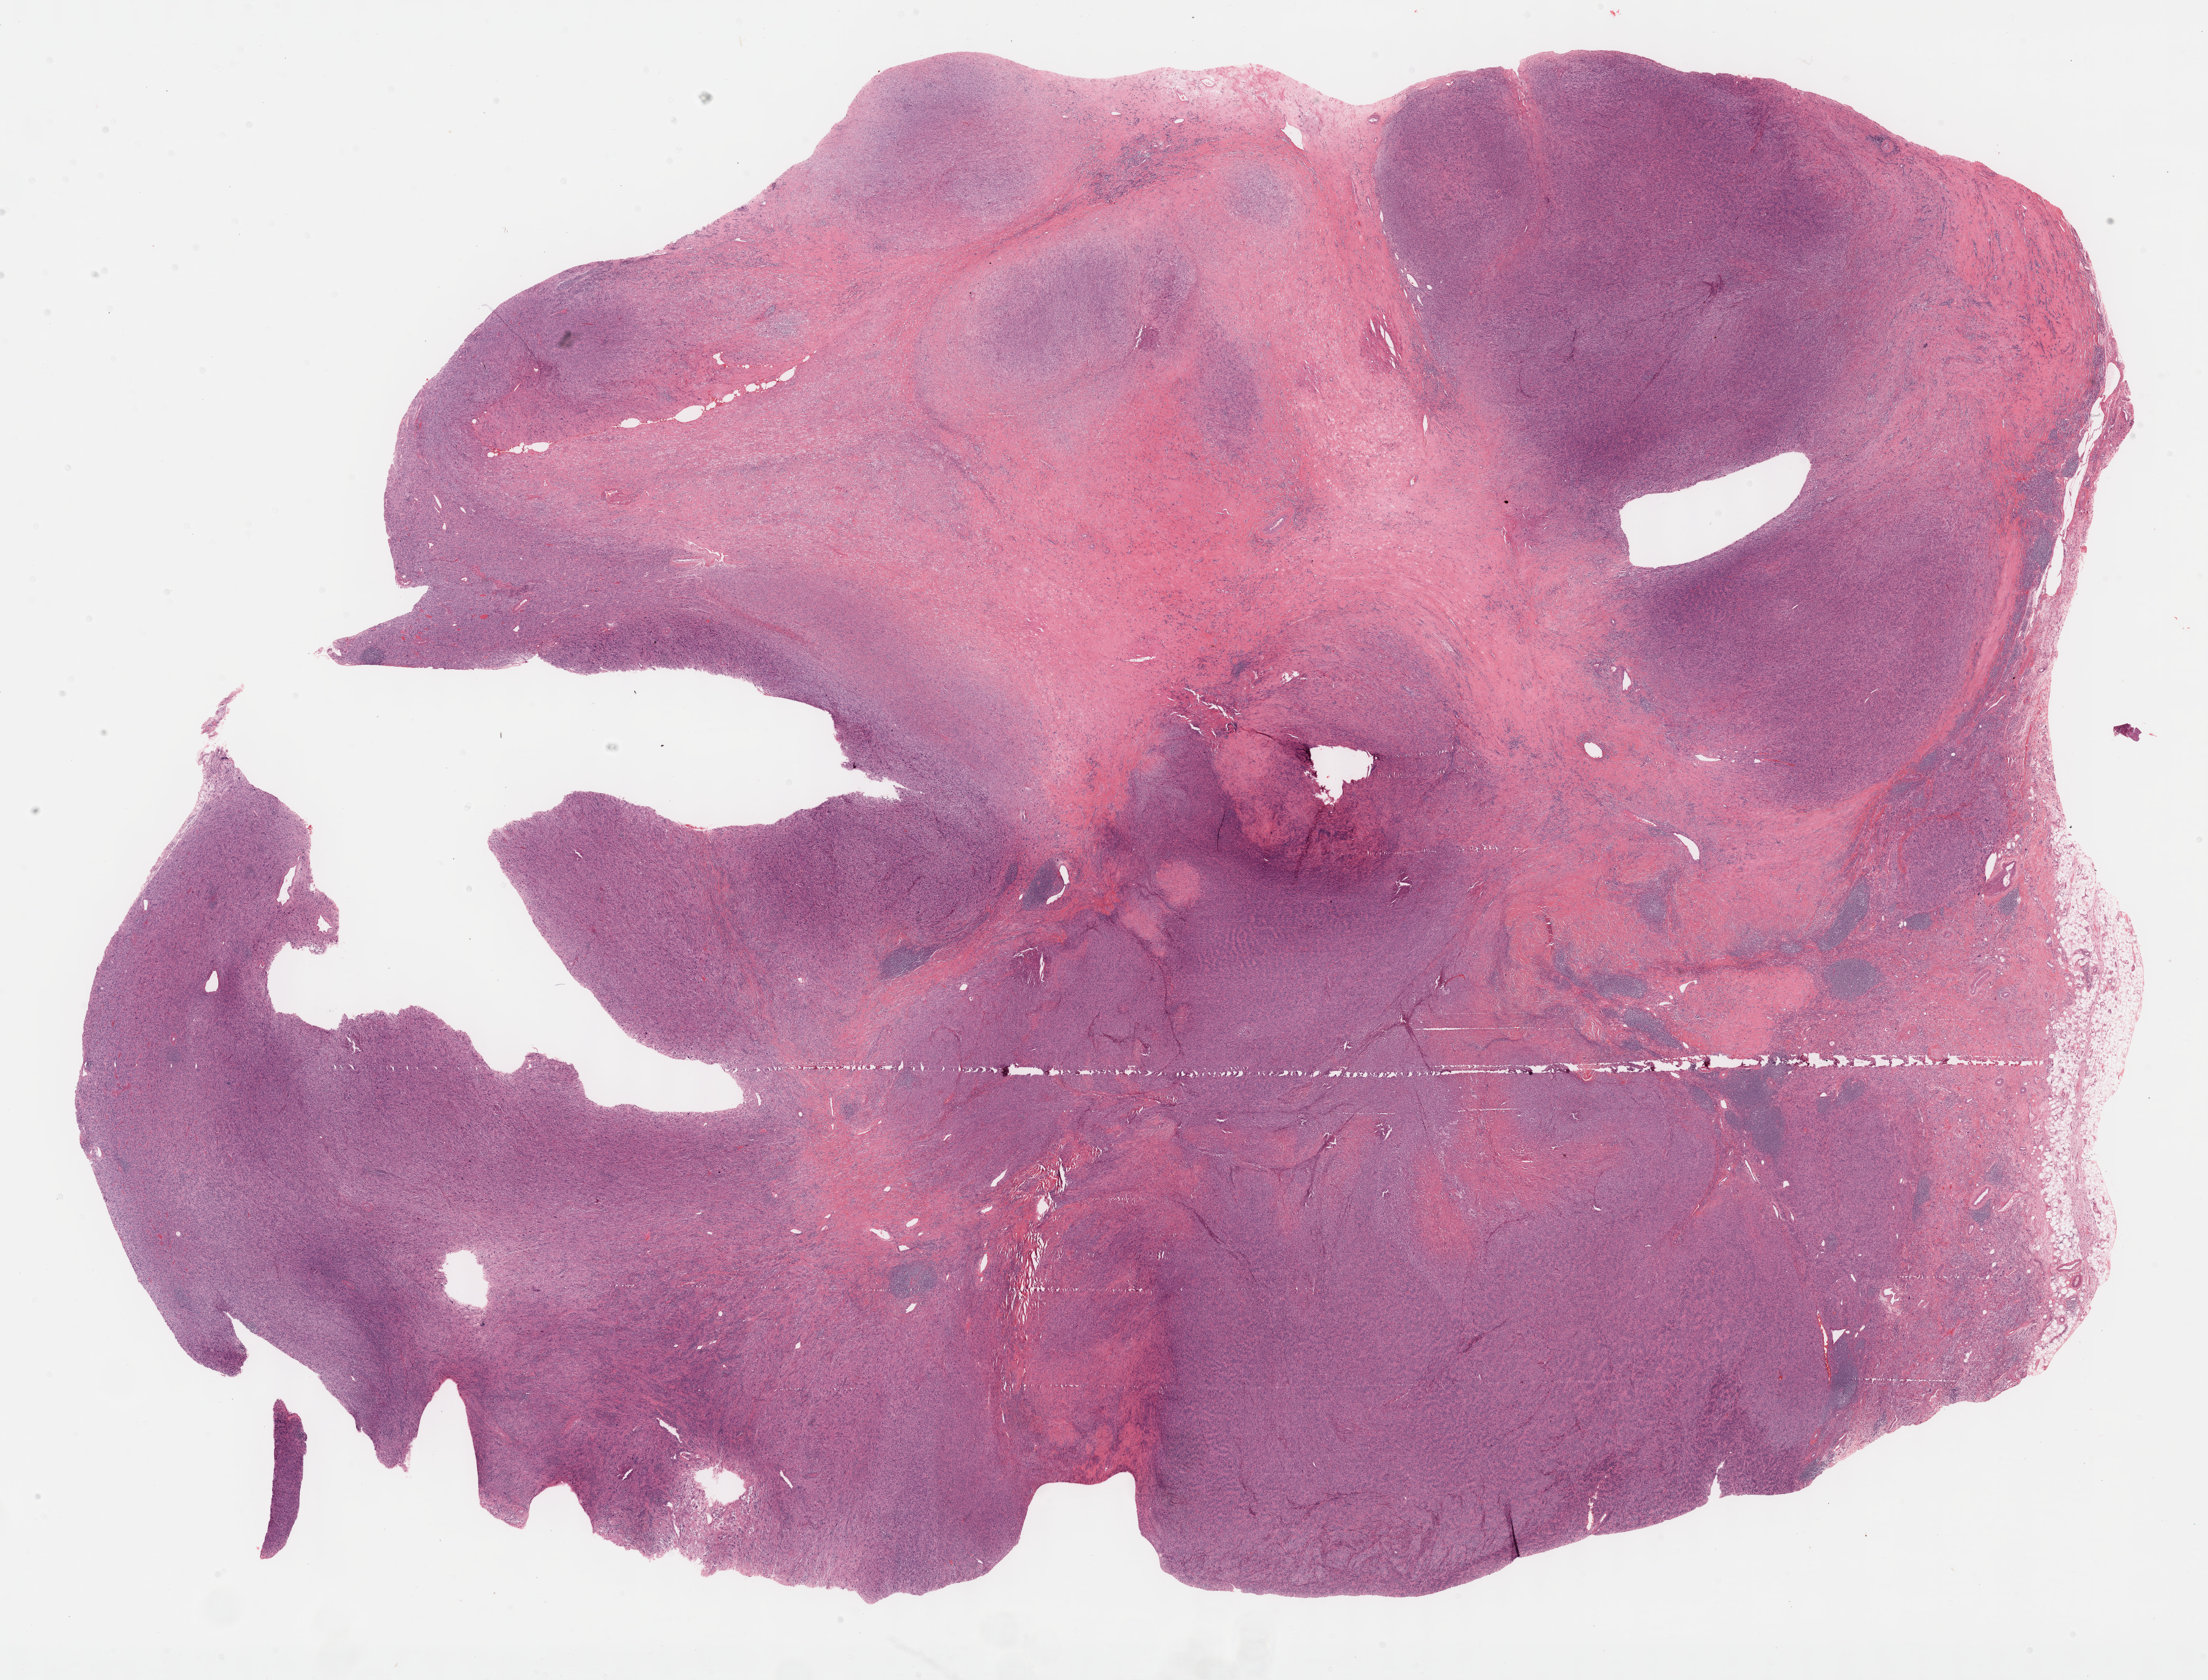
H&E-stained whole-slide image — whole scanned area (about 29.2 x 22.2 mm) shown as a low-resolution overview. FFPE section. Connective, subcutaneous and other soft tissues, primary tumour sample. Female, age 73 years at initial diagnosis.
Histologic diagnosis: Dedifferentiated liposarcoma (connective, subcutaneous and other soft tissues of lower limb and hip).